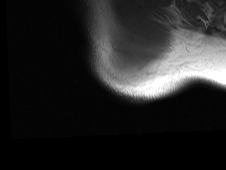
MRI of an extremity soft-tissue mass, one axial slice; slice 60 of 81 in the series (ordered by position); MR volume resampled by the dataset authors to the PET/CT grid (not the native acquisition matrix); 226 × 170 image matrix, field of view 221 × 166 mm. Male patient. From the clinical record (not read from this slice): histological type: pleiomorphic spindle cell undifferentiated; grade: high; site of the primary tumour: right parascapusular.
Structures marked on this image (expert contour drawn on MRI and transferred to this co-registered scan by the dataset authors):
- gross tumour volume including surrounding oedema: bounding box <106,54,166,89> (left, top, right, bottom; pixels)
- gross tumour volume (mass): <108,54,141,85>